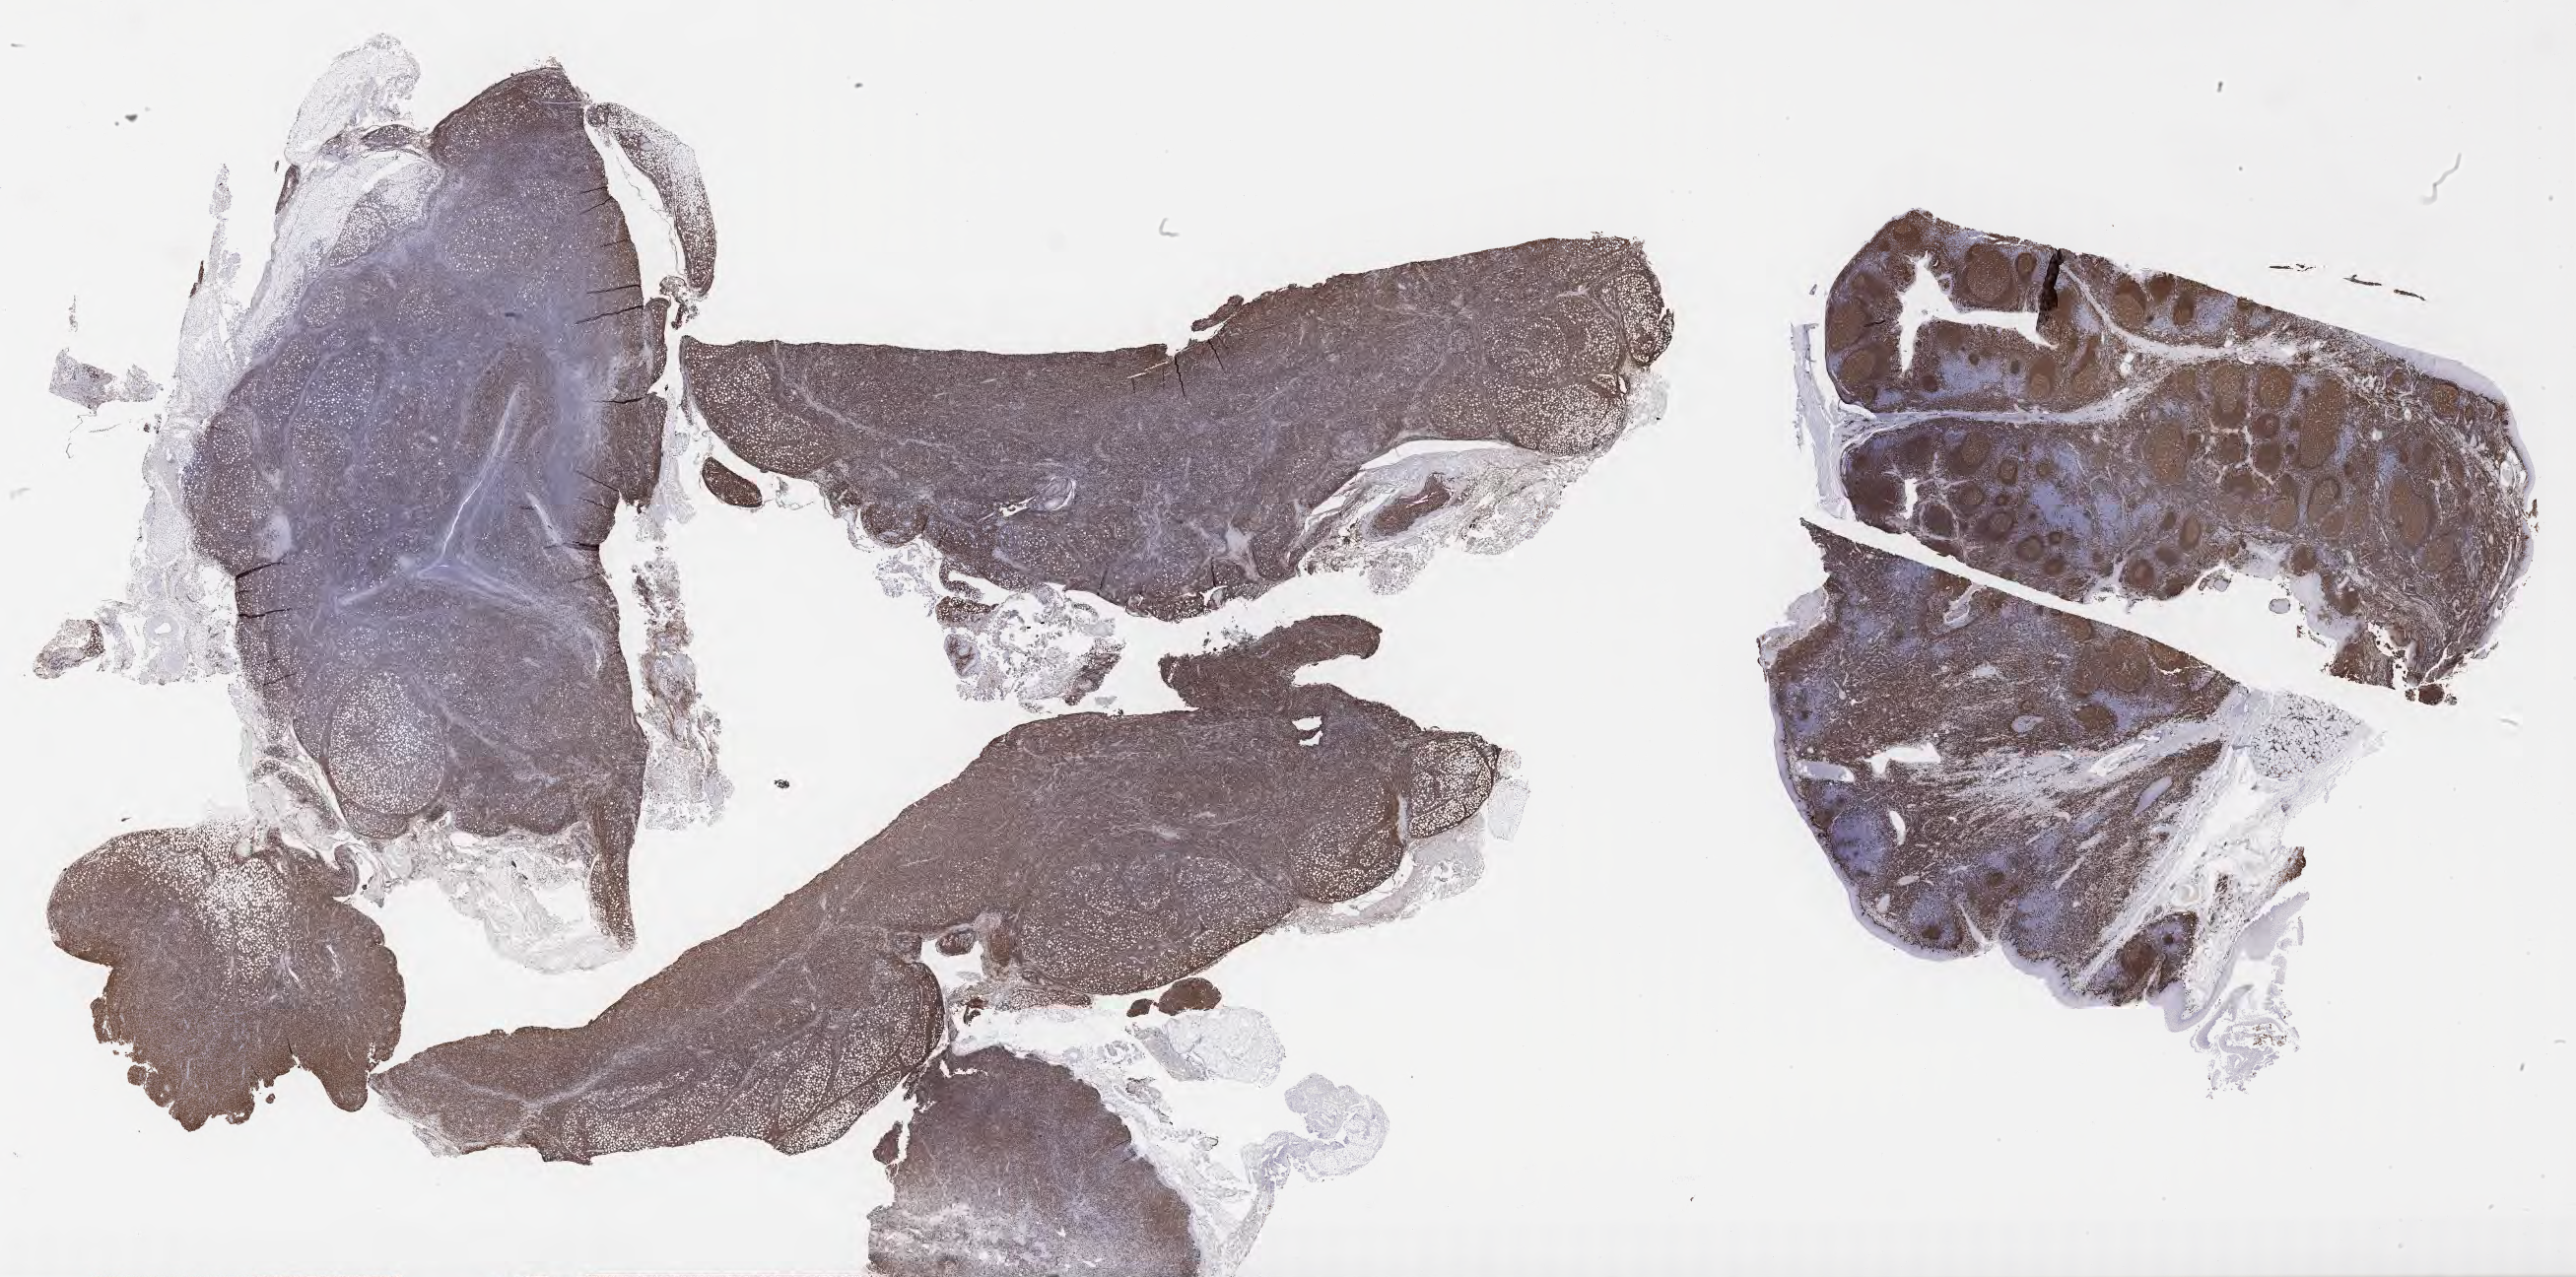
Immunohistochemistry (IHC) whole-slide image stained for CD79a, shown as a low-resolution overview of the whole scanned area (about 42.3 x 21.0 mm); tumor tissue; site: lymph node. Patient male; age 68 years.
Diagnosis: Diffuse large B-cell lymphoma, NOS.